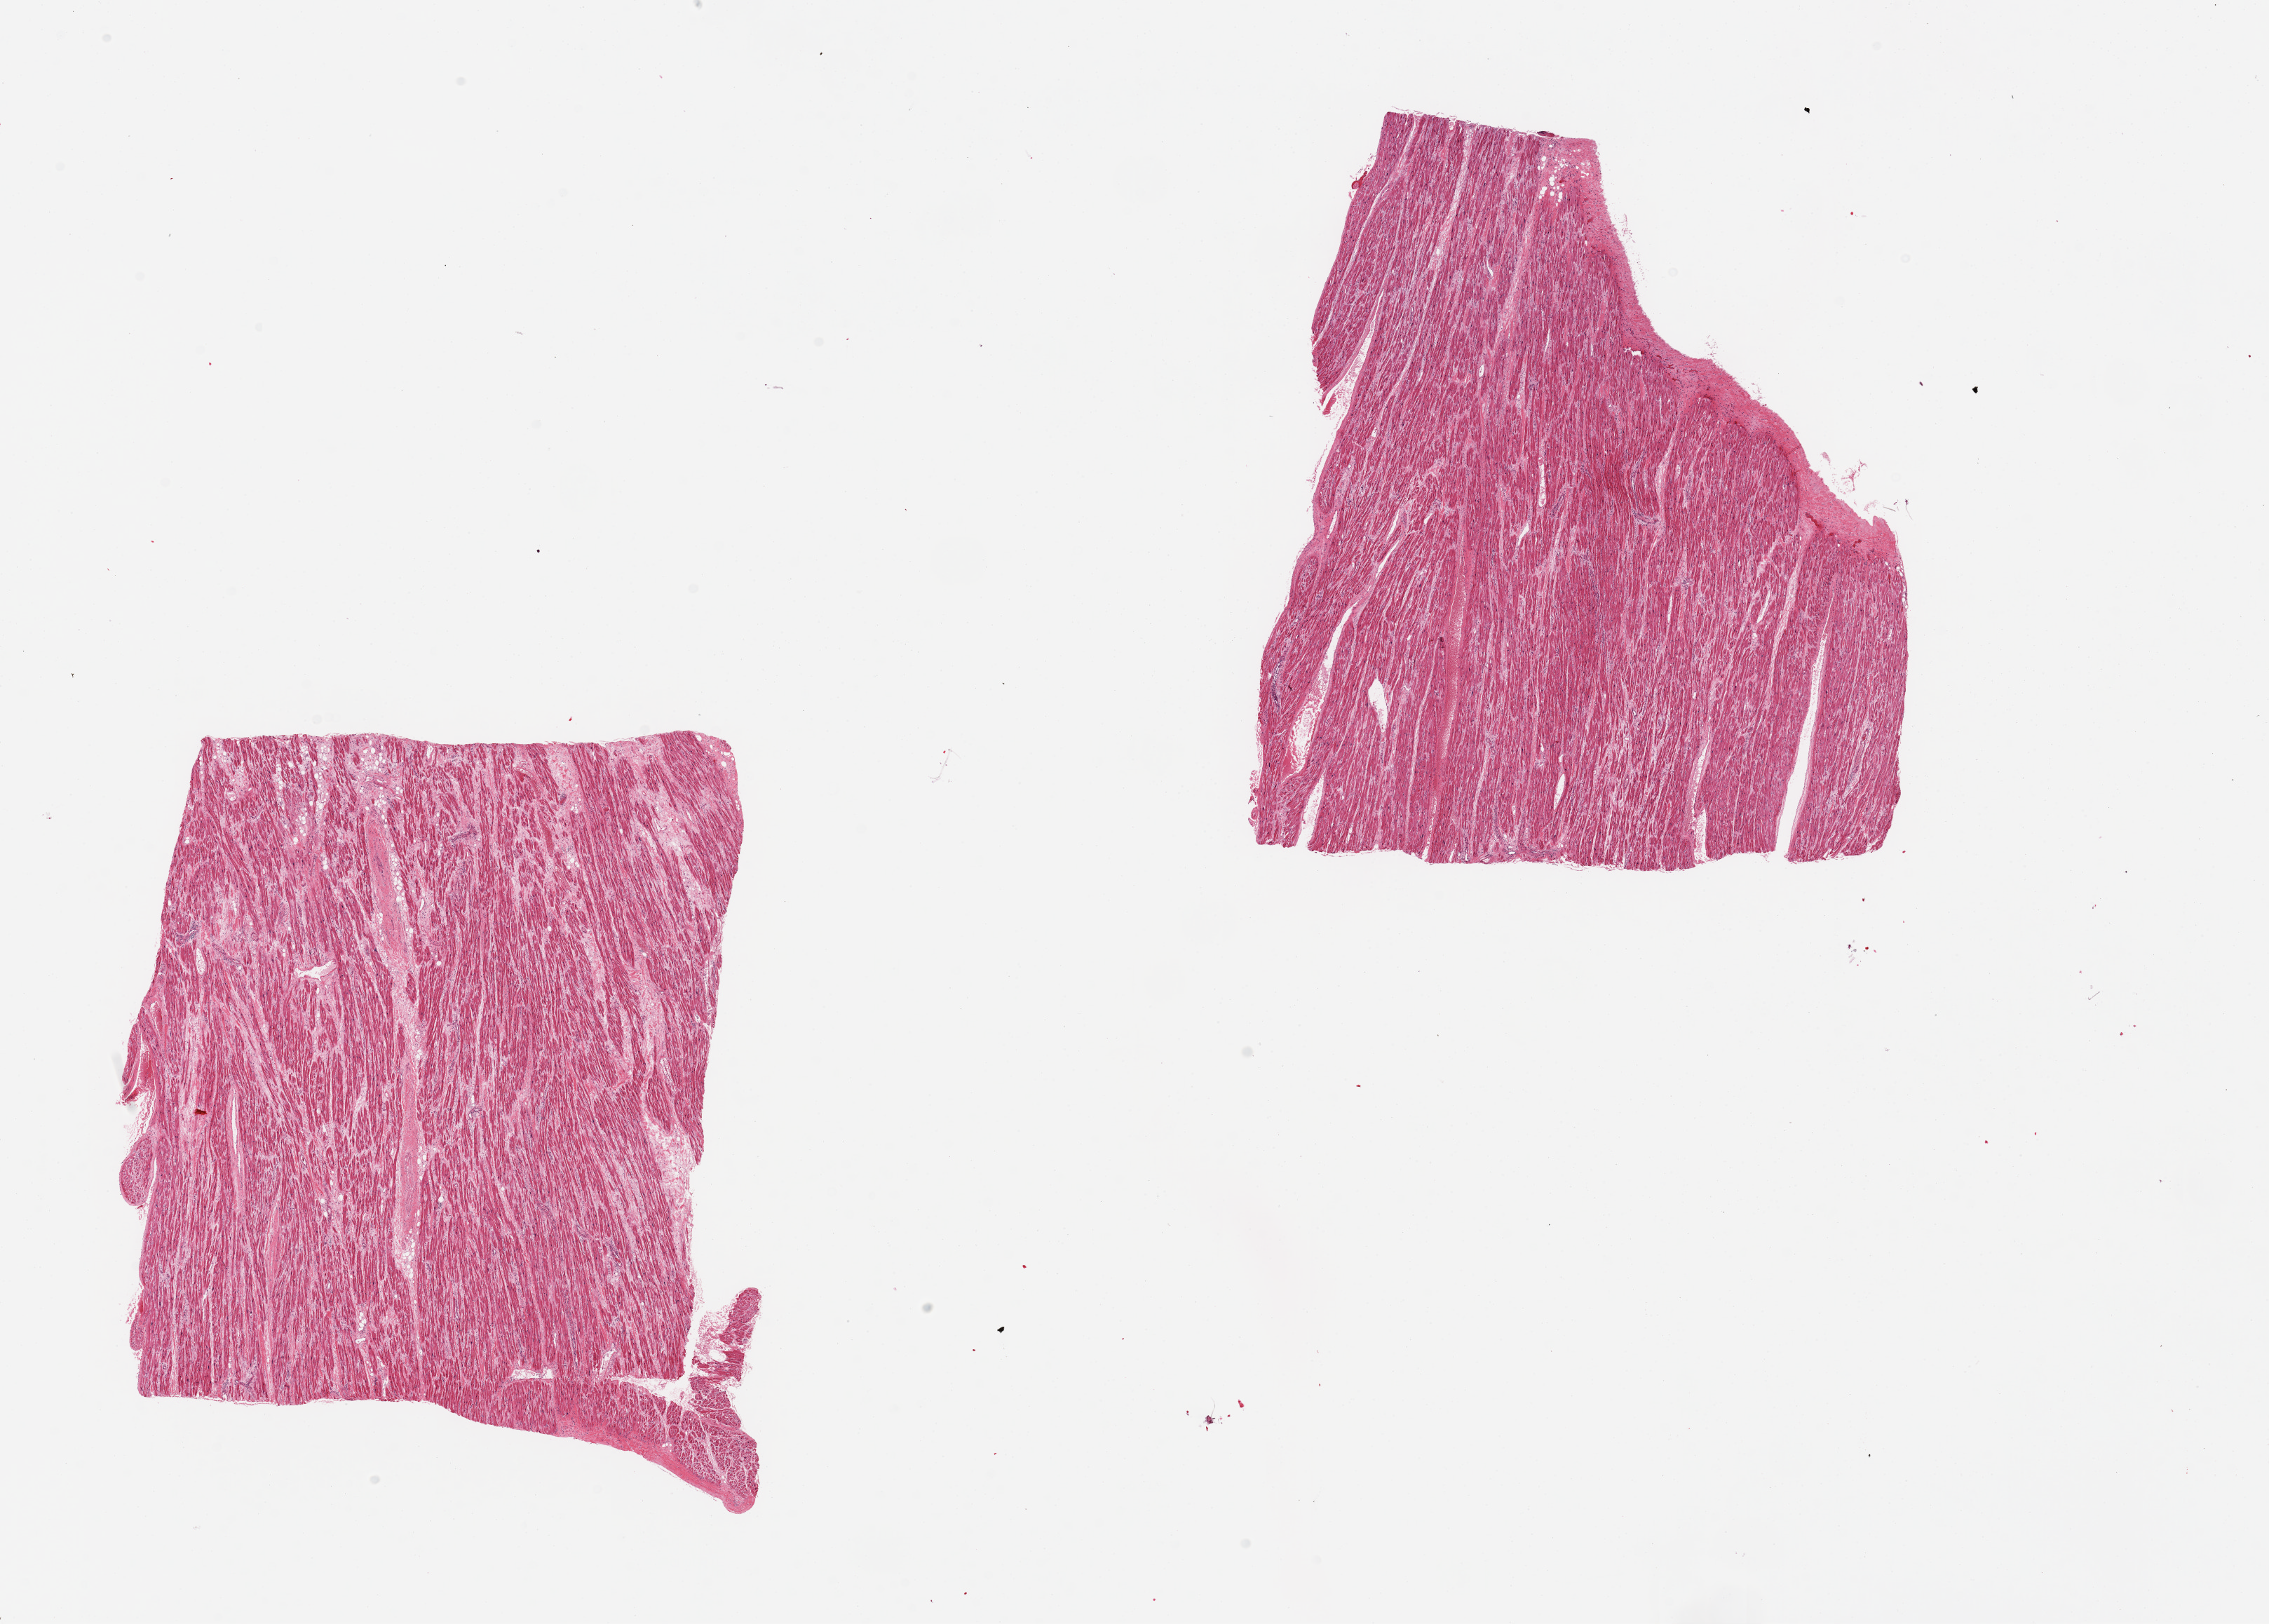
H&E whole-slide image — a low-resolution overview of the entire scanned area, about 25.6 x 18.3 mm (slide scanned at 20x); PAXgene-fixed, paraffin-embedded tissue; section of auricular appendage (target tissue); donor tissue sample. Donor sex: female.
Reviewer comment on this tissue sample: 2 pieces, no abnormalities.